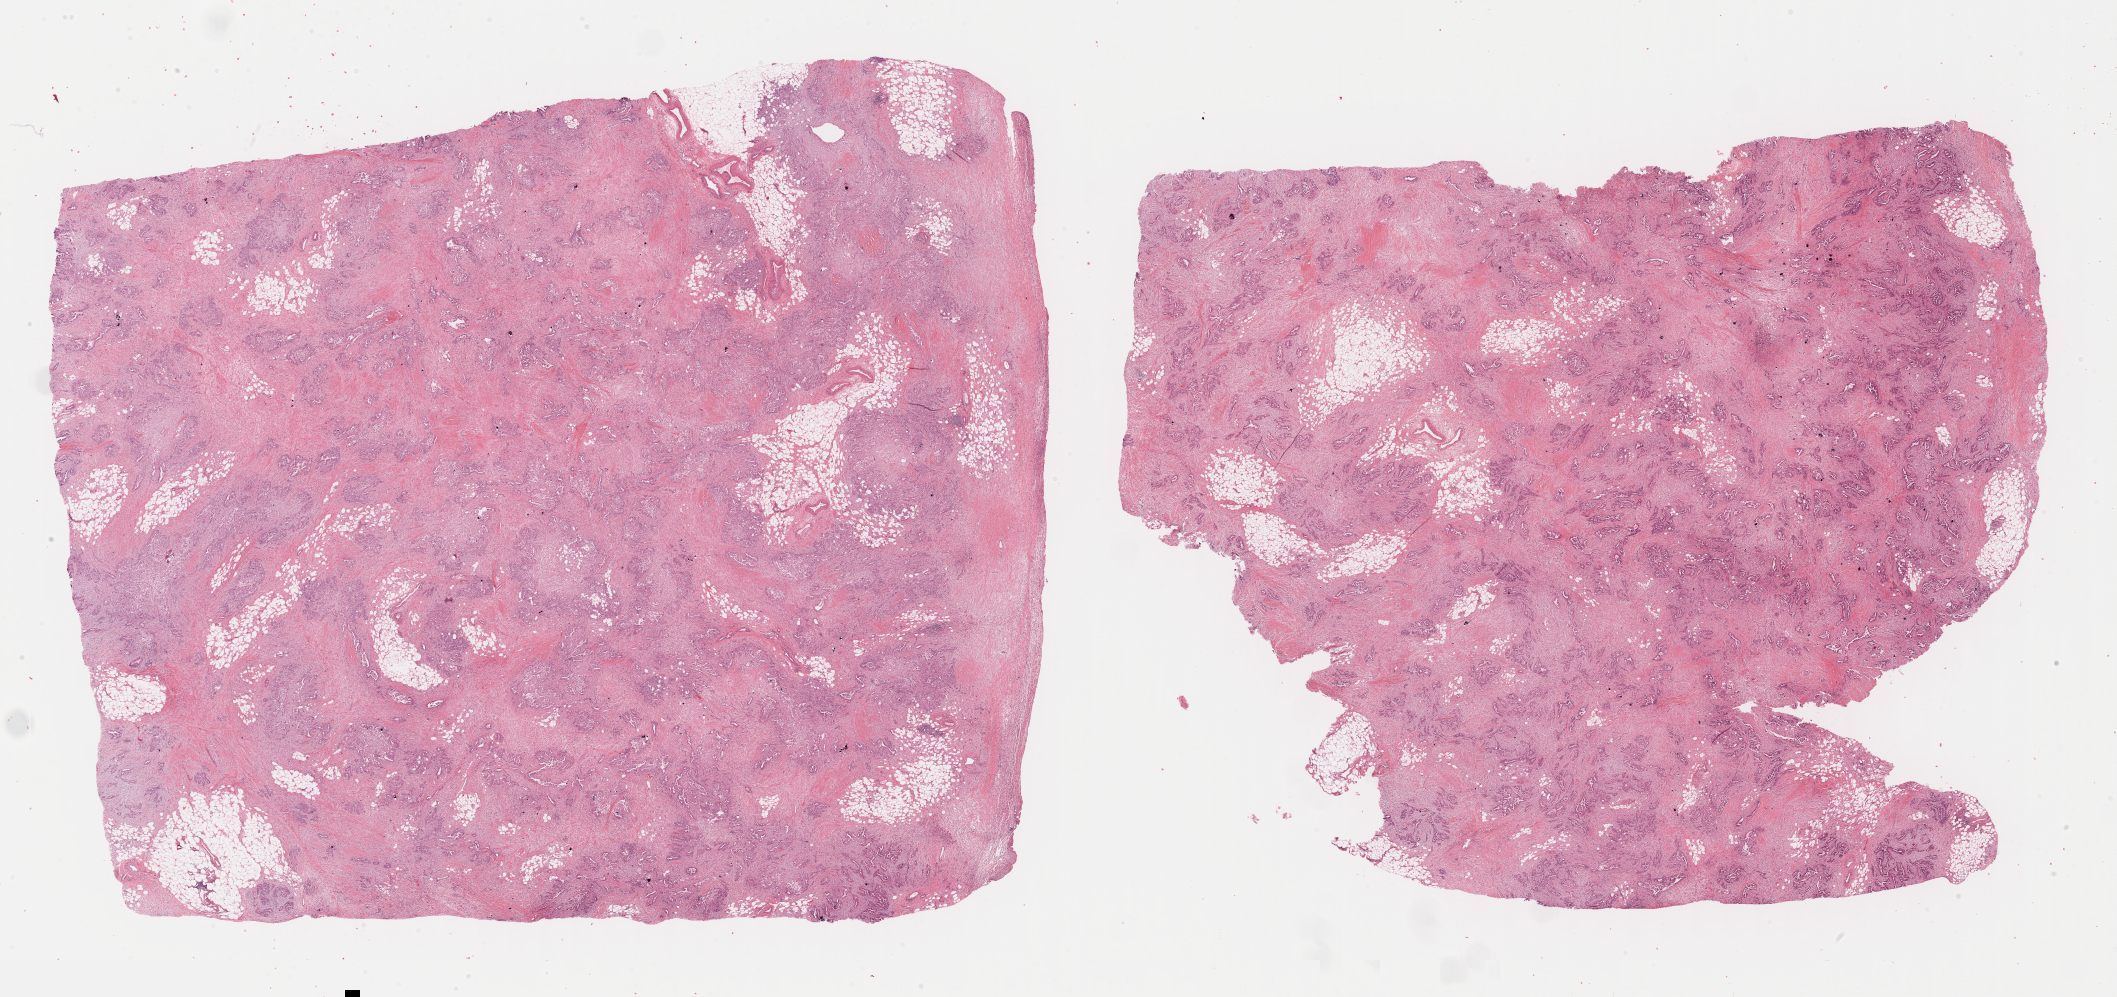
H&E-stained whole-slide image — shown as a low-resolution overview of the whole scanned area (about 34.2 x 16.1 mm, acquisition: 40x scan), formalin-fixed paraffin-embedded (FFPE) diagnostic section, ovary, primary tumour sample. Female patient; age at initial diagnosis 62 years. Histologic grade: G3 (poorly differentiated).
* laterality: bilateral
* FIGO stage: IV
* histologic diagnosis: Serous cystadenocarcinoma, NOS